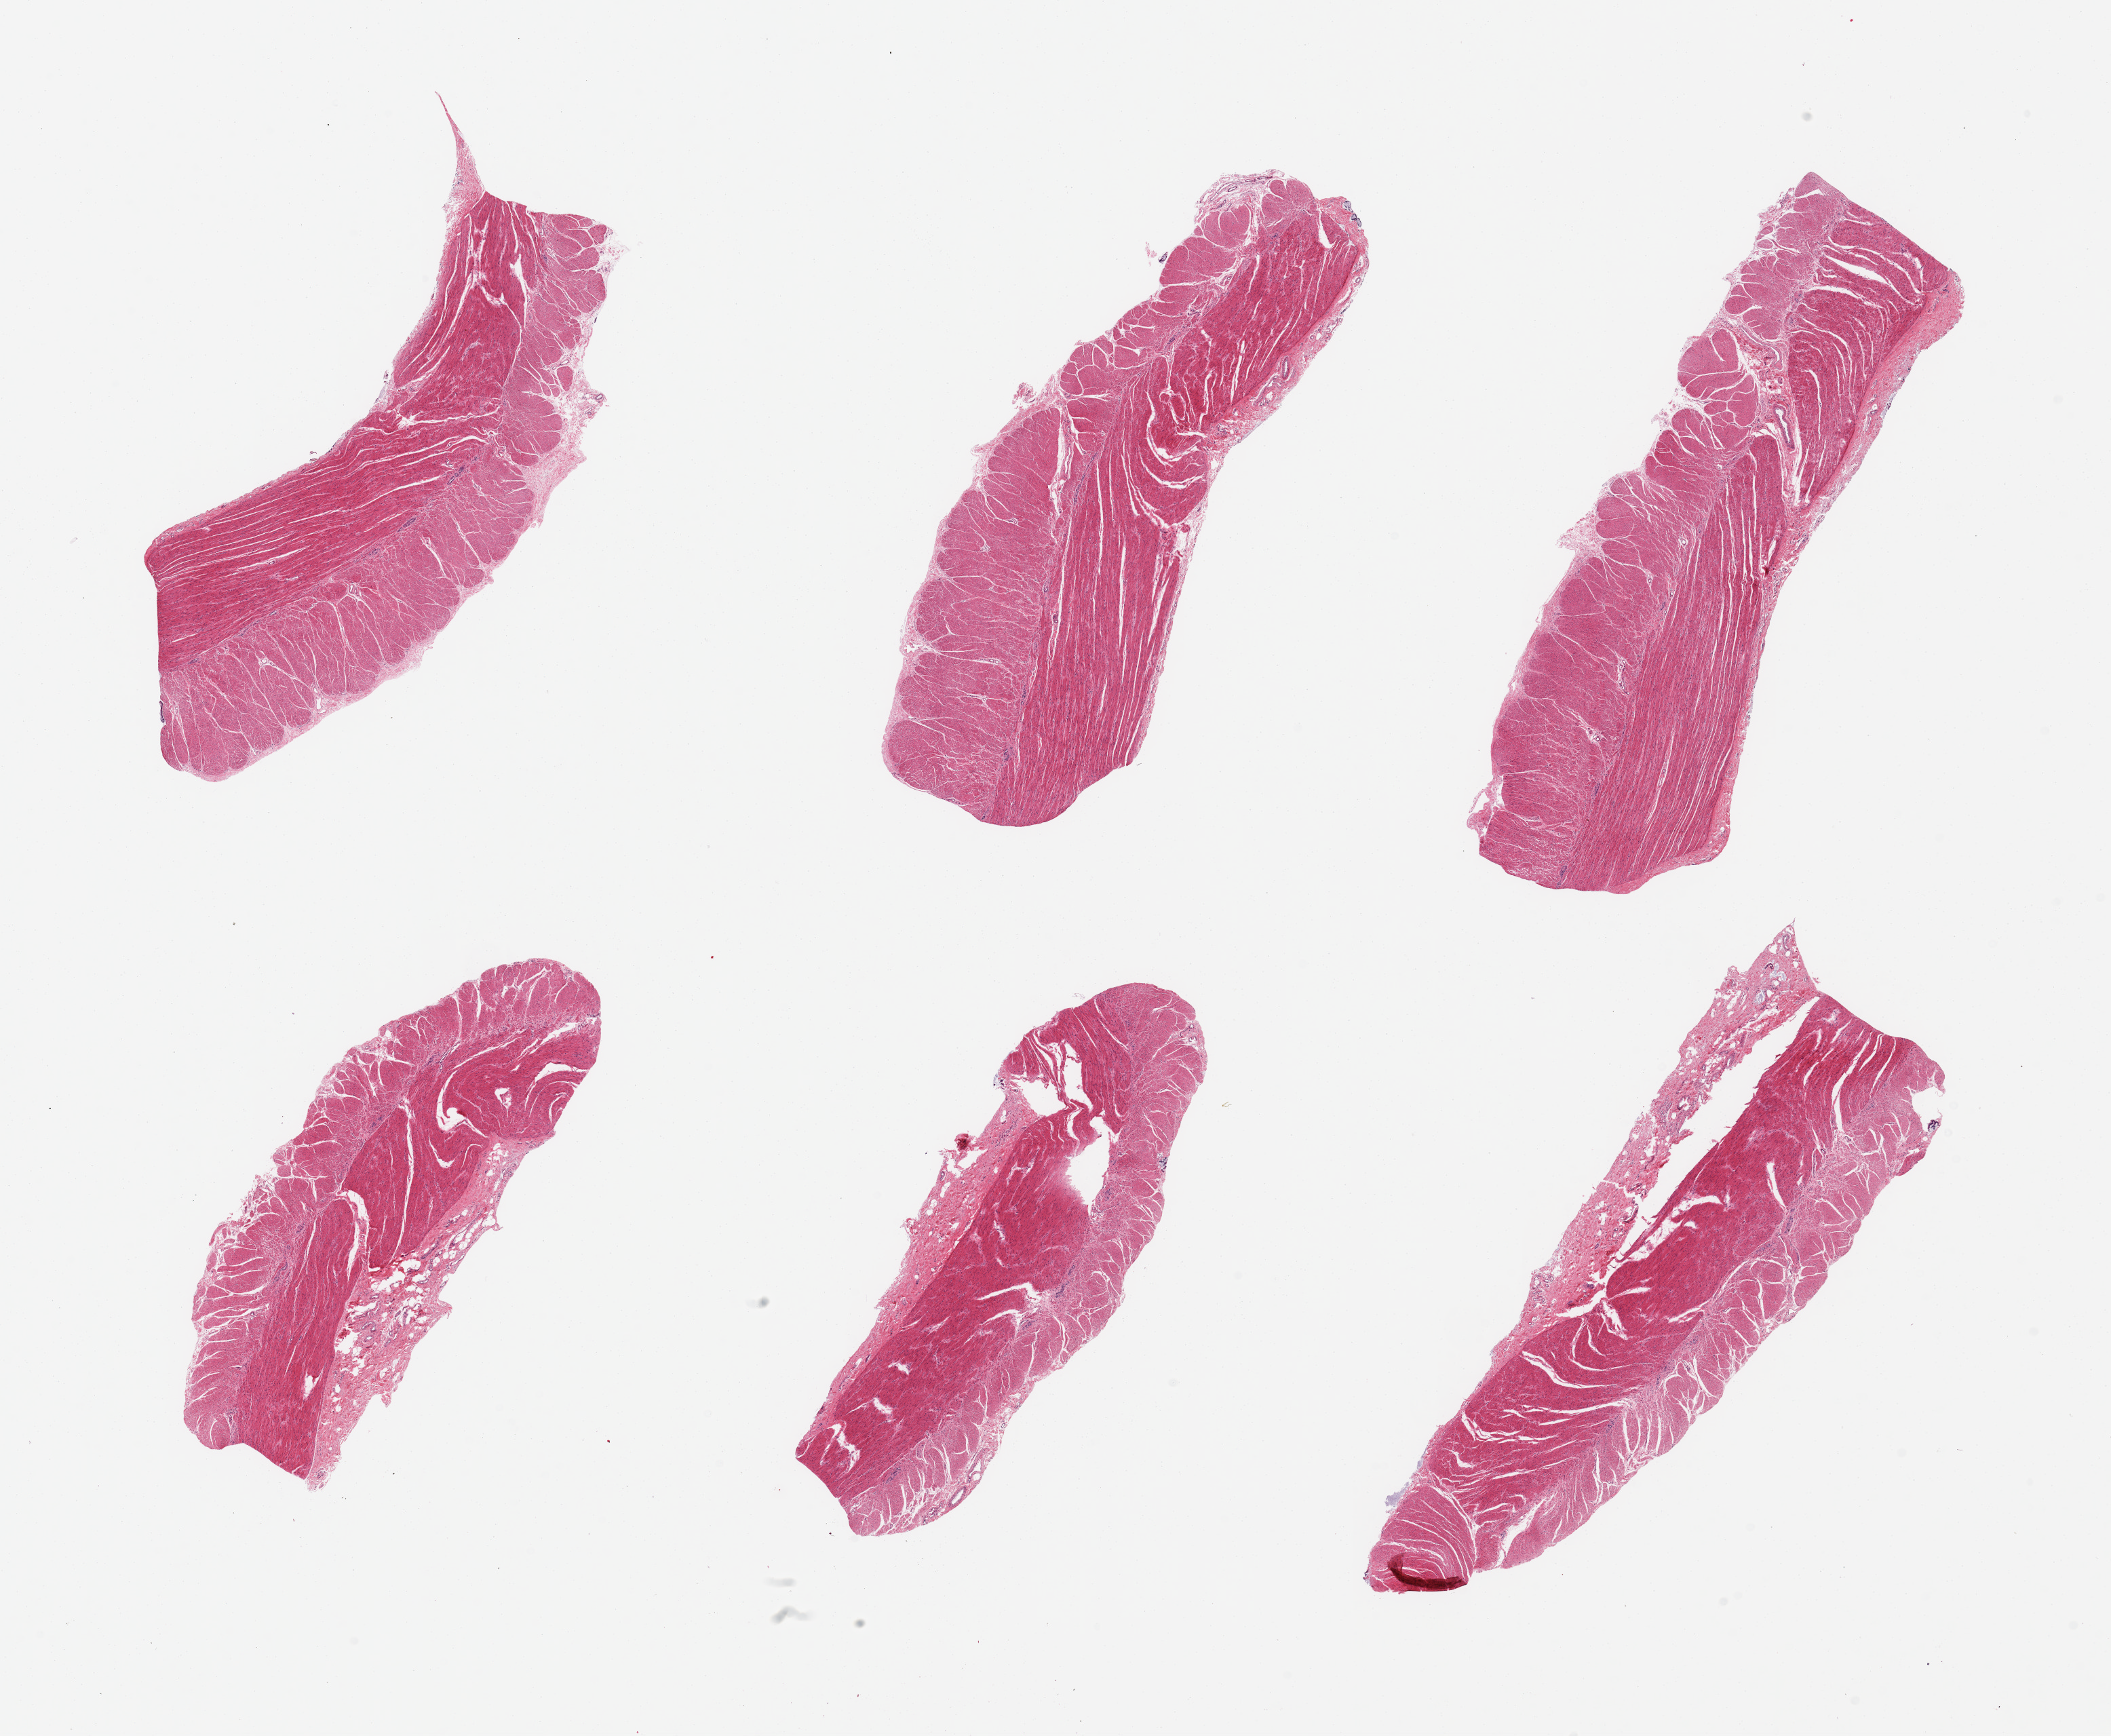
Digitized H&E-stained section, low-resolution overview of the scanned area, about 24.6 x 20.2 mm. PAXgene-fixed, paraffin-embedded tissue. Section of sigmoid colon (target tissue). Tissue donor sample. Female donor.
Reviewer comment on this tissue sample: 6 pieces; essentially well trimmed target muscularis.